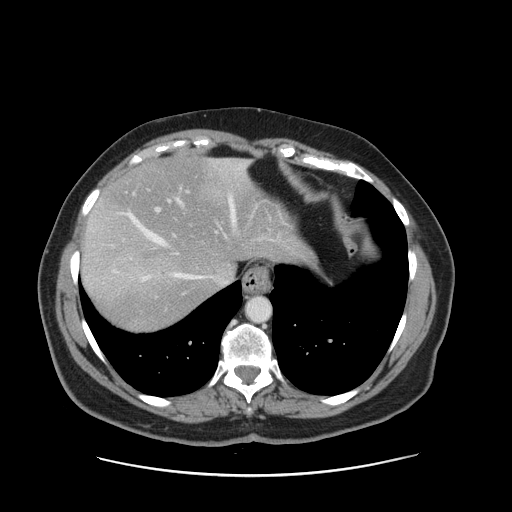
Contrast-enhanced abdominal CT, one axial slice. Position 126 of 161 along the scan axis. 120 kVp. Intravenous contrast given. Soft-tissue window (W 400 / L 40 HU). 2.5 mm slice thickness. 512 × 512 image matrix. Female patient, age 62 years. From the clinical record (not read from this slice): diagnosis: colorectal cancer liver metastases, imaged before liver resection; multiple liver metastases: no; largest metastasis: 2.5 cm; chemotherapy before resection: yes.
Outlined on this slice (manually delineated by an expert):
- hepatic veins: box from (x=113, y=161) to (x=248, y=281) px
- liver: (x=82, y=159)–(x=301, y=329)
- planned liver remnant (the part of the liver to remain after resection): (x=95, y=159)–(x=301, y=279)
- portal vein (with intrahepatic branches): (x=155, y=190)–(x=189, y=237)